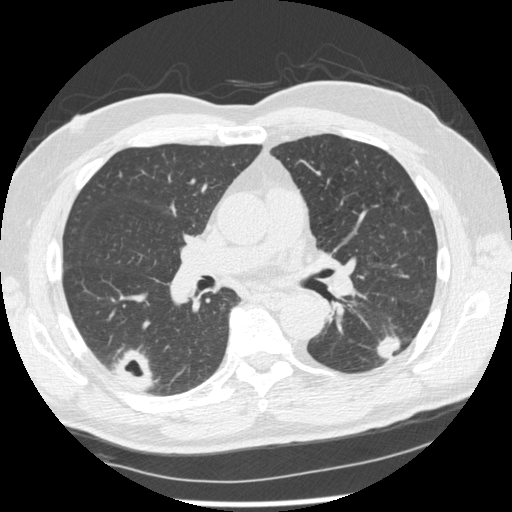
Chest CT (low-dose screening protocol), one axial image, second screening round (one year after baseline), lung window (W 1500 / L -600 HU), standard (soft-tissue) reconstruction kernel (STANDARD), slice 113 of 227 in the series, 512 × 512 image matrix, field of view 360 × 360 mm. Male participant, aged 74 years at enrolment. Former smoker at enrolment.
Expert reader's lesion annotation, bounding box (x1, y1, x2, y2) in pixels: (370, 315, 421, 368). The screening reader recorded 7 non-calcified nodules or masses ≥4 mm on this exam (right upper lobe, right lower lobe, right upper lobe, right lower lobe, left lower lobe, left upper lobe, left upper lobe); which of them this box marks is not recorded. Participant outcome: lung cancer diagnosed 43 days after this screen — squamous cell carcinoma, NOS, left lower lobe, well differentiated (G1), stage IA (AJCC 6th edition), 28 mm at pathology.